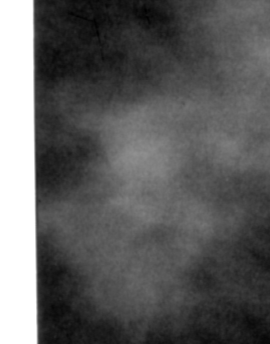
Region of interest cut from a scanned film mammogram (one marked finding); right breast; MLO view.
Mass, shape focal asymmetric density, margins ill defined; BI-RADS assessment category 4; pathology (as recorded): benign.